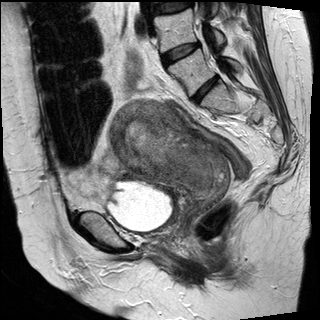
Pelvic MRI for cervical cancer, one sagittal slice; slice 17 of 30 in the series (ordered by position); T2-weighted; 1.5 T; TE 89 ms, TR 3810 ms; 4 mm slice thickness; 320 × 320 image matrix, field of view 260 × 260 mm. Patient: female, 62 years.
Outlined on this slice (manually delineated by an expert):
- uterus and cervix: bounding box [x1, y1, x2, y2] px = [108, 98, 232, 200]